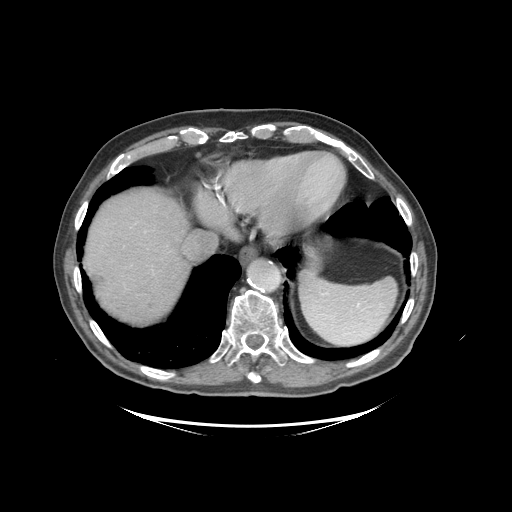
Contrast-enhanced abdominal CT (liver protocol), one axial slice. Slice 84 of 99 in the series (ordered by position). Soft-tissue window (W 400 / L 40 HU). 512 × 512 image matrix. Case-level facts recorded for this patient, not image findings: diagnosis: hepatocellular carcinoma (patient treated with transarterial chemoembolisation; whether this scan precedes or follows treatment is not stated here); TNM stage (as recorded): Stage-I.
Annotated regions visible in this slice (semi-automatic segmentation, software-assisted and operator-edited):
- abdominal aorta: bounding box <249,261,279,290> (left, top, right, bottom; pixels)
- liver parenchyma outside the tumour (the mass and vessels are separate outlines, so this box may not span the whole liver): <84,190,202,322>